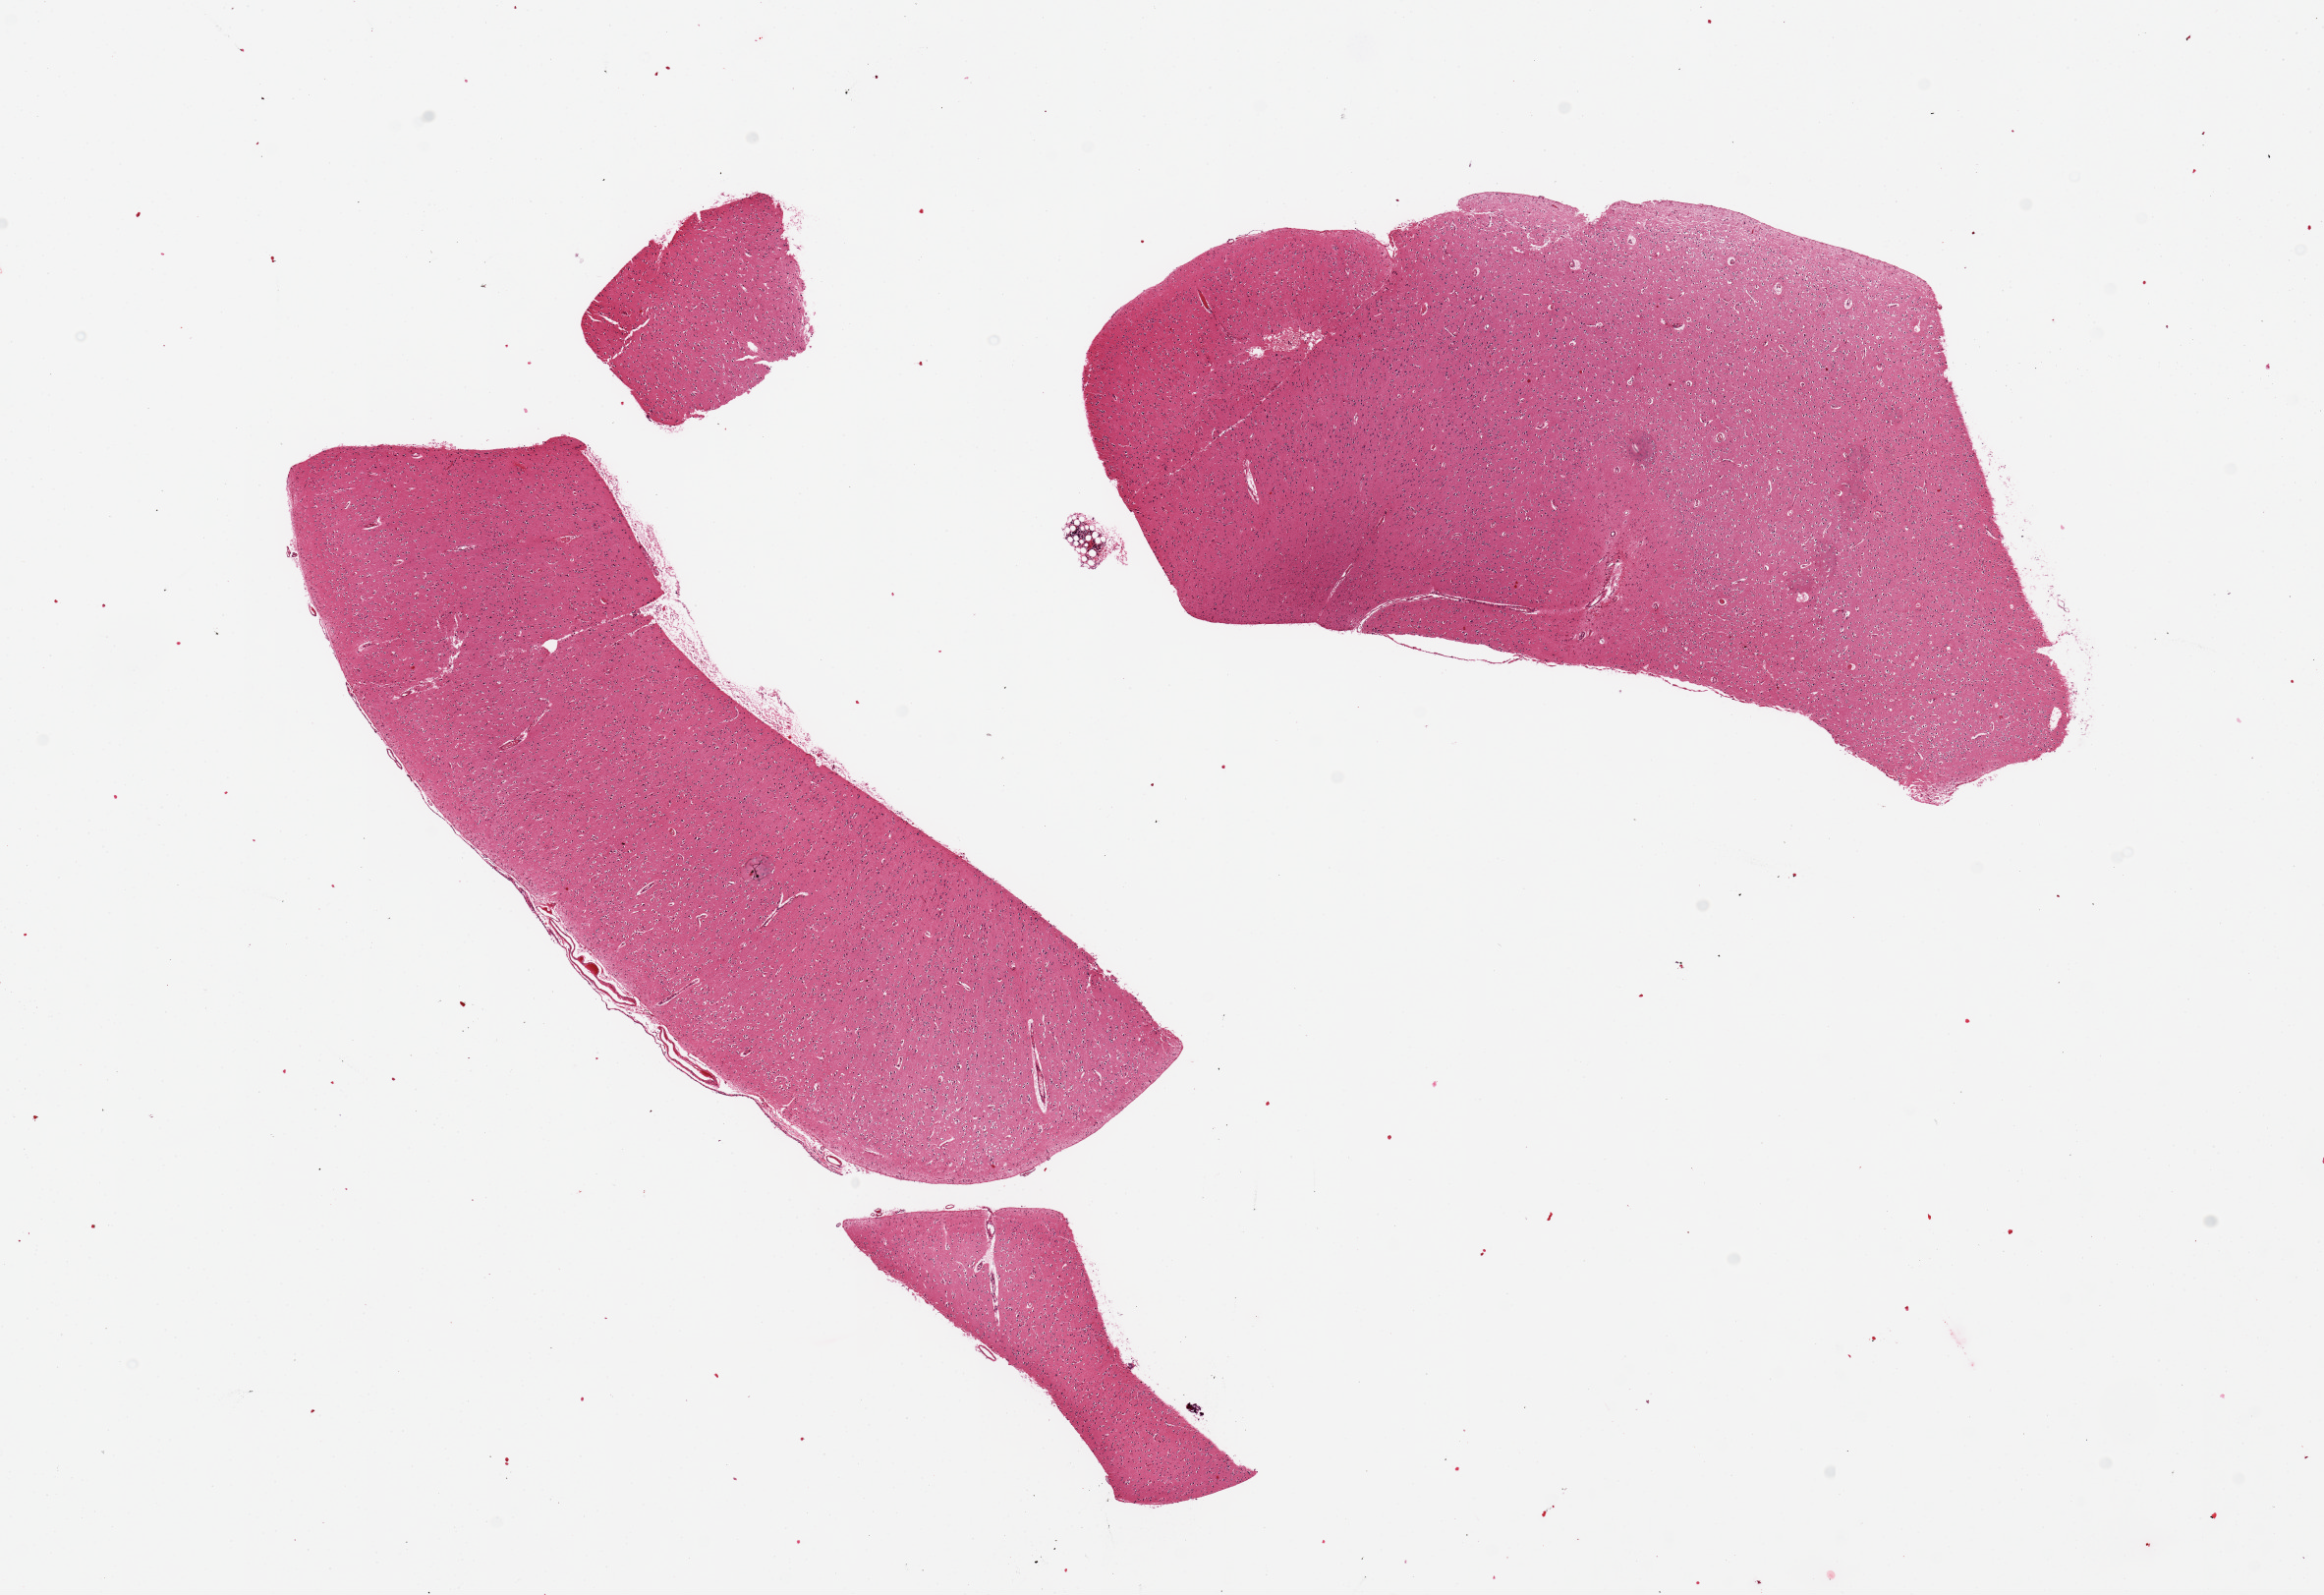
H&E whole-slide image — low-resolution overview of the scanned area, about 18.7 x 12.8 mm, PAXgene-fixed paraffin-embedded (PFPE) section, target tissue: cerebral cortex, tissue donor sample. Female donor.
Review note (as recorded): 2 pieces (fragmented), no abnormalities.